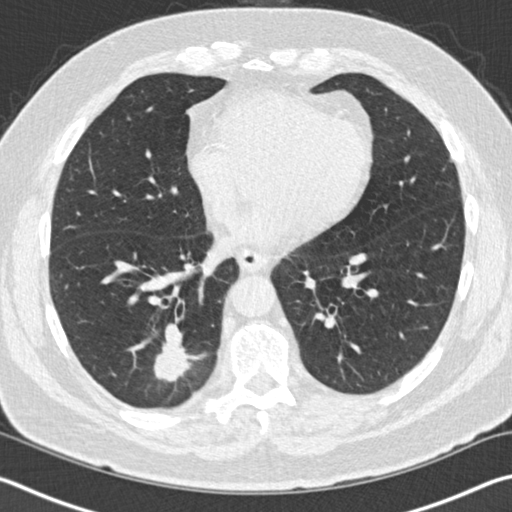
Low-dose screening chest CT, one axial slice. Slice 44 of 141 in the series (ordered by position). Reconstruction kernel B30f. Lung window (W 1500 / L -600 HU). 2 mm slice thickness. 512 × 512 image matrix.
Annotated regions visible in this slice (expert manual segmentation):
- lesion 1 (tumor, lower lobe of right lung): box from (x=154, y=323) to (x=192, y=382) px